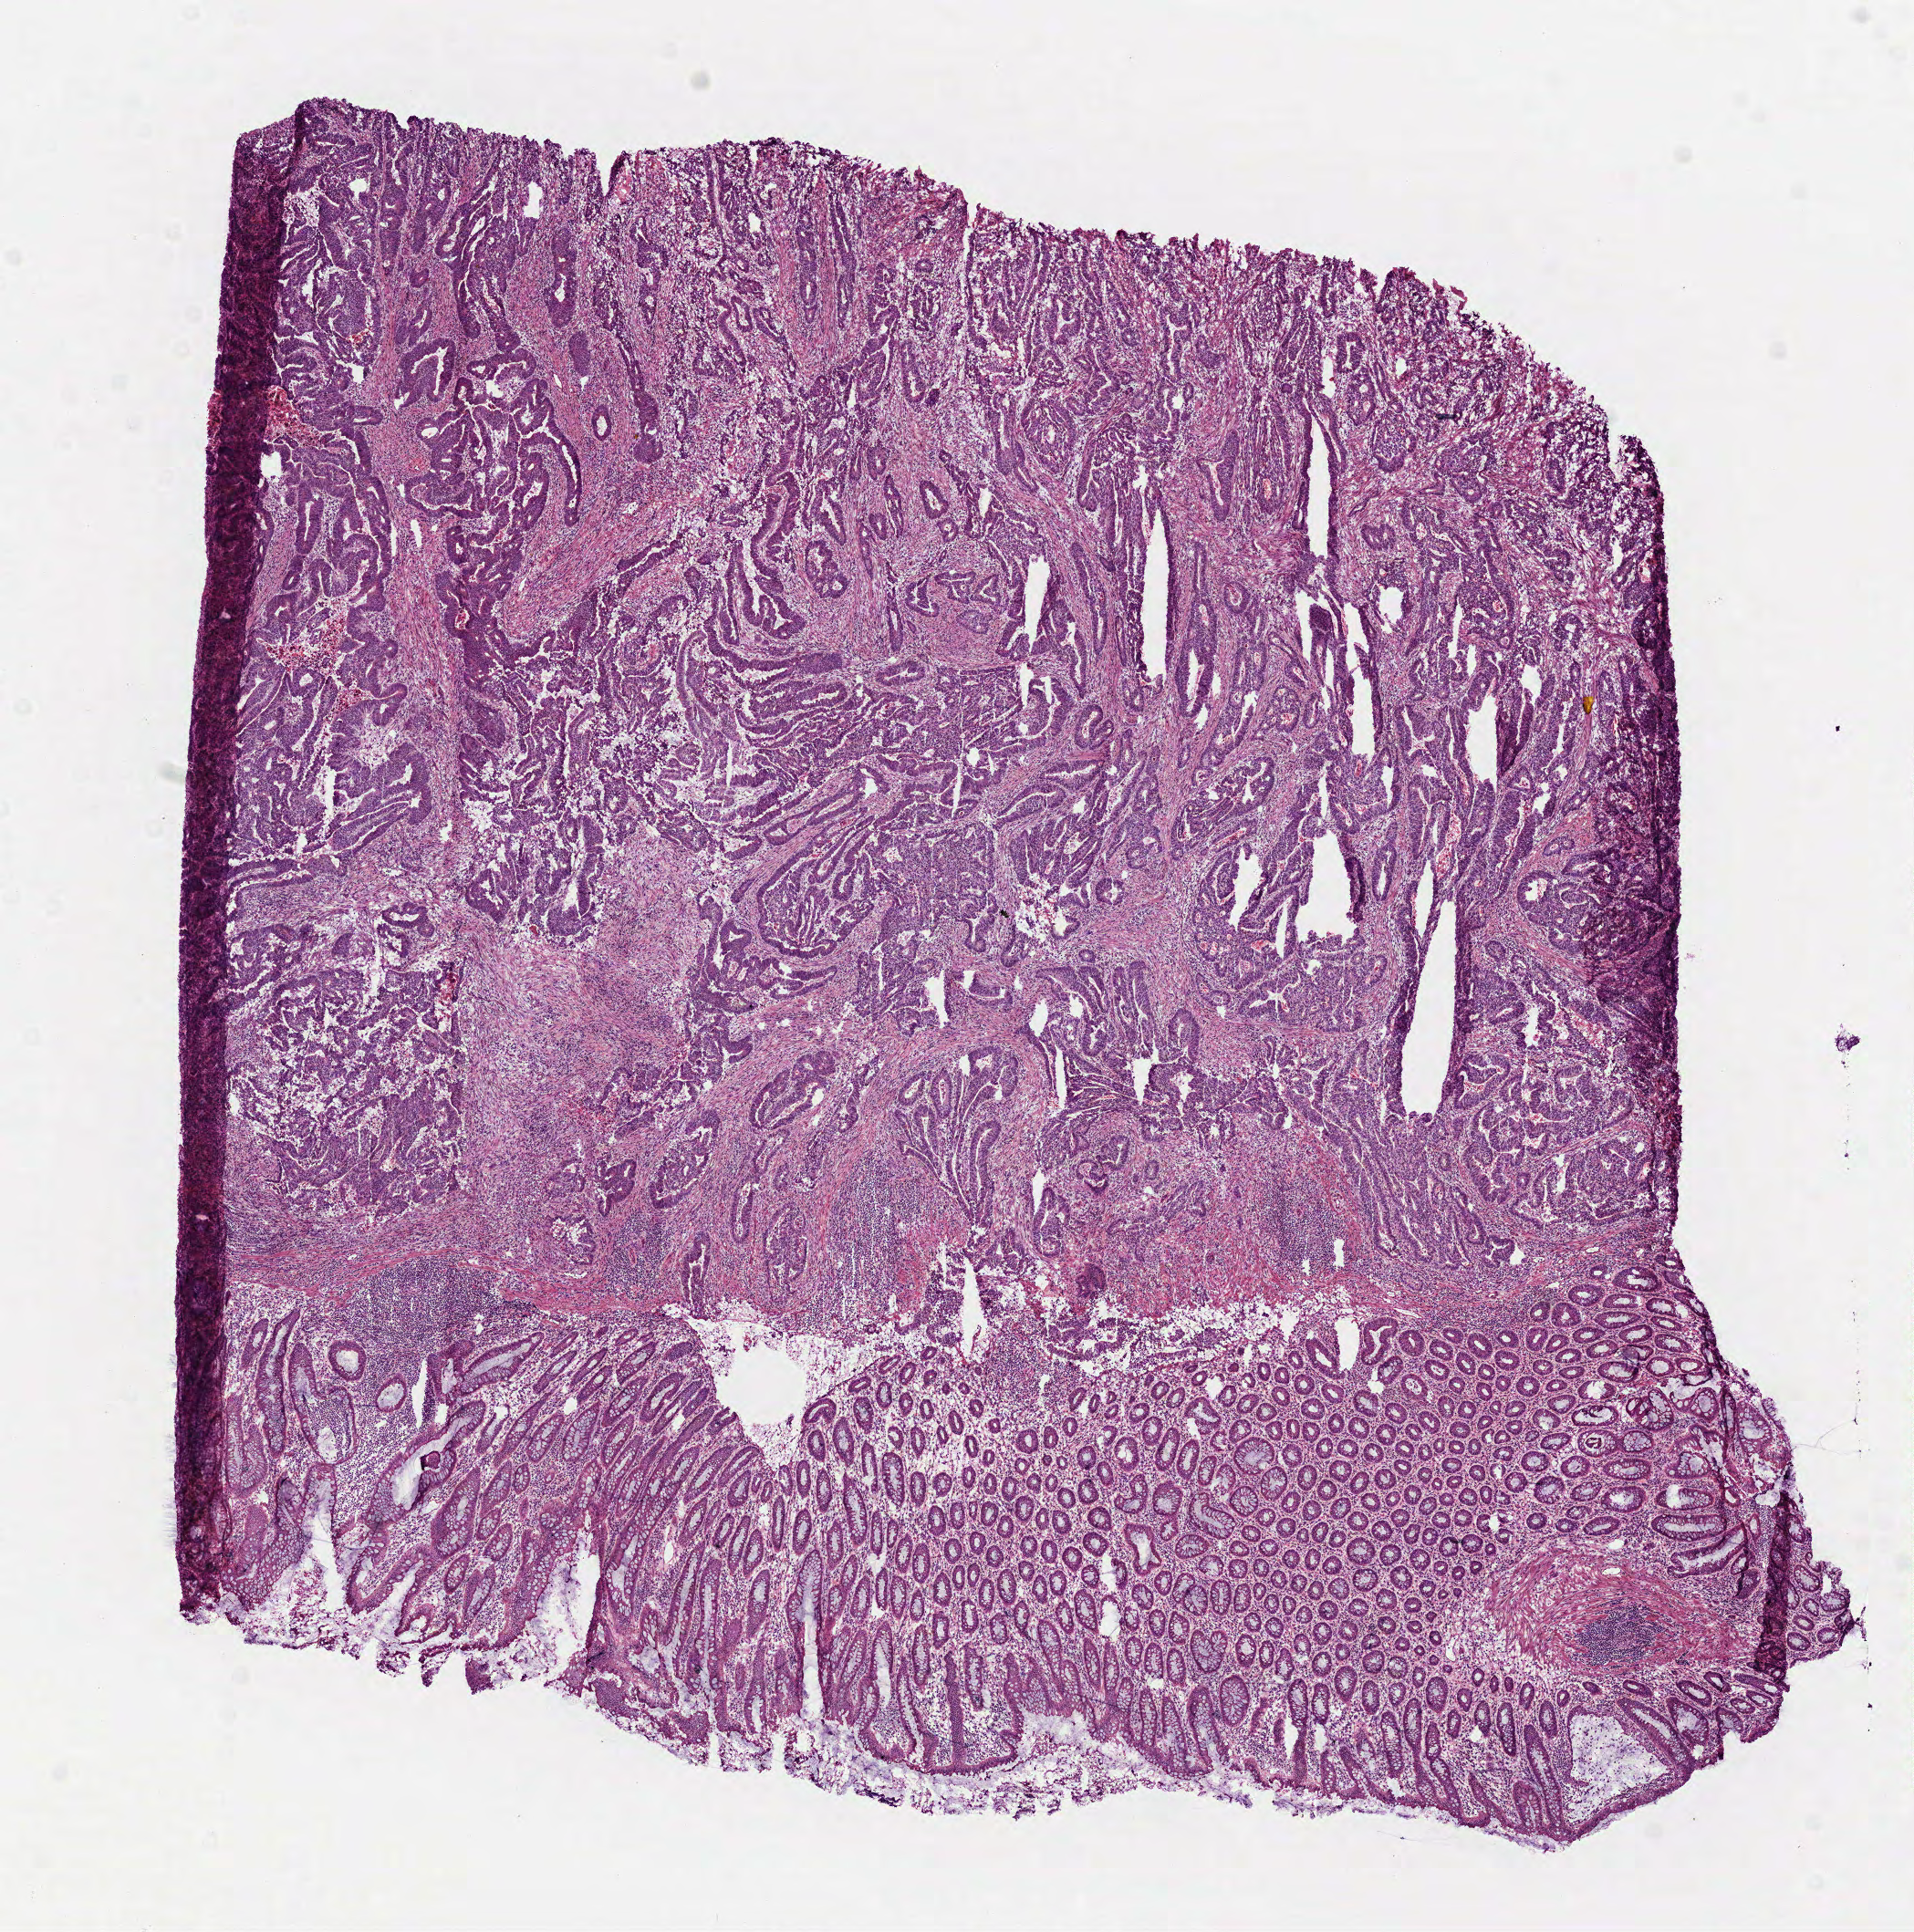
Whole-slide histology image, H&E-stained, a low-resolution overview of the entire scanned area, about 8.5 x 8.5 mm, frozen section from the top of the tissue portion, rectum, primary tumour sample. Patient: female, age at initial diagnosis 79 years. Slide review estimates, as recorded: tumour cells 70%, tumour nuclei 71%, normal cells 29%, stromal cells 0%, necrosis 1%. Infiltration values recorded for this section: lymphocyte infiltration 15%, monocyte infiltration 0%, neutrophil infiltration 2%.
- lymph nodes positive (case pathology): 0 of 21 examined
- diagnosis: Adenocarcinoma, NOS (rectosigmoid junction)